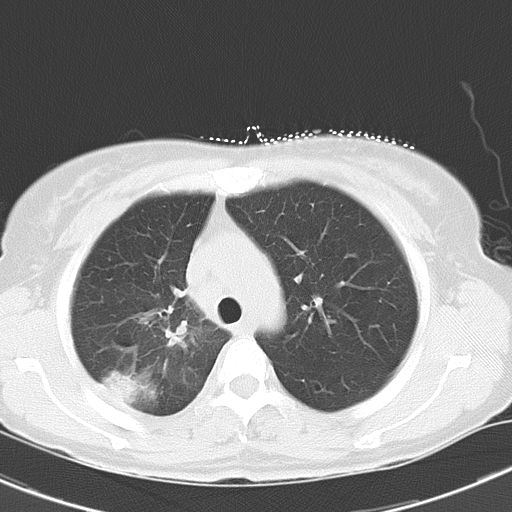
Chest CT, one axial slice; position 22 of 29 along the scan axis; 120 kVp; lung window (W 1500 / L -600 HU); 8 mm slice thickness; 512 × 512 image matrix, field of view 300 × 300 mm. Female patient, age 47 years. Case-level facts recorded for this patient, not image findings: clinical TNM (as recorded): T1c N3 M0.
Outlined on this slice (bounding box drawn by a radiologist):
- lung tumour (recorded histology: adenocarcinoma): bounding box (x1, y1, x2, y2) in pixels: (103, 369, 150, 409)